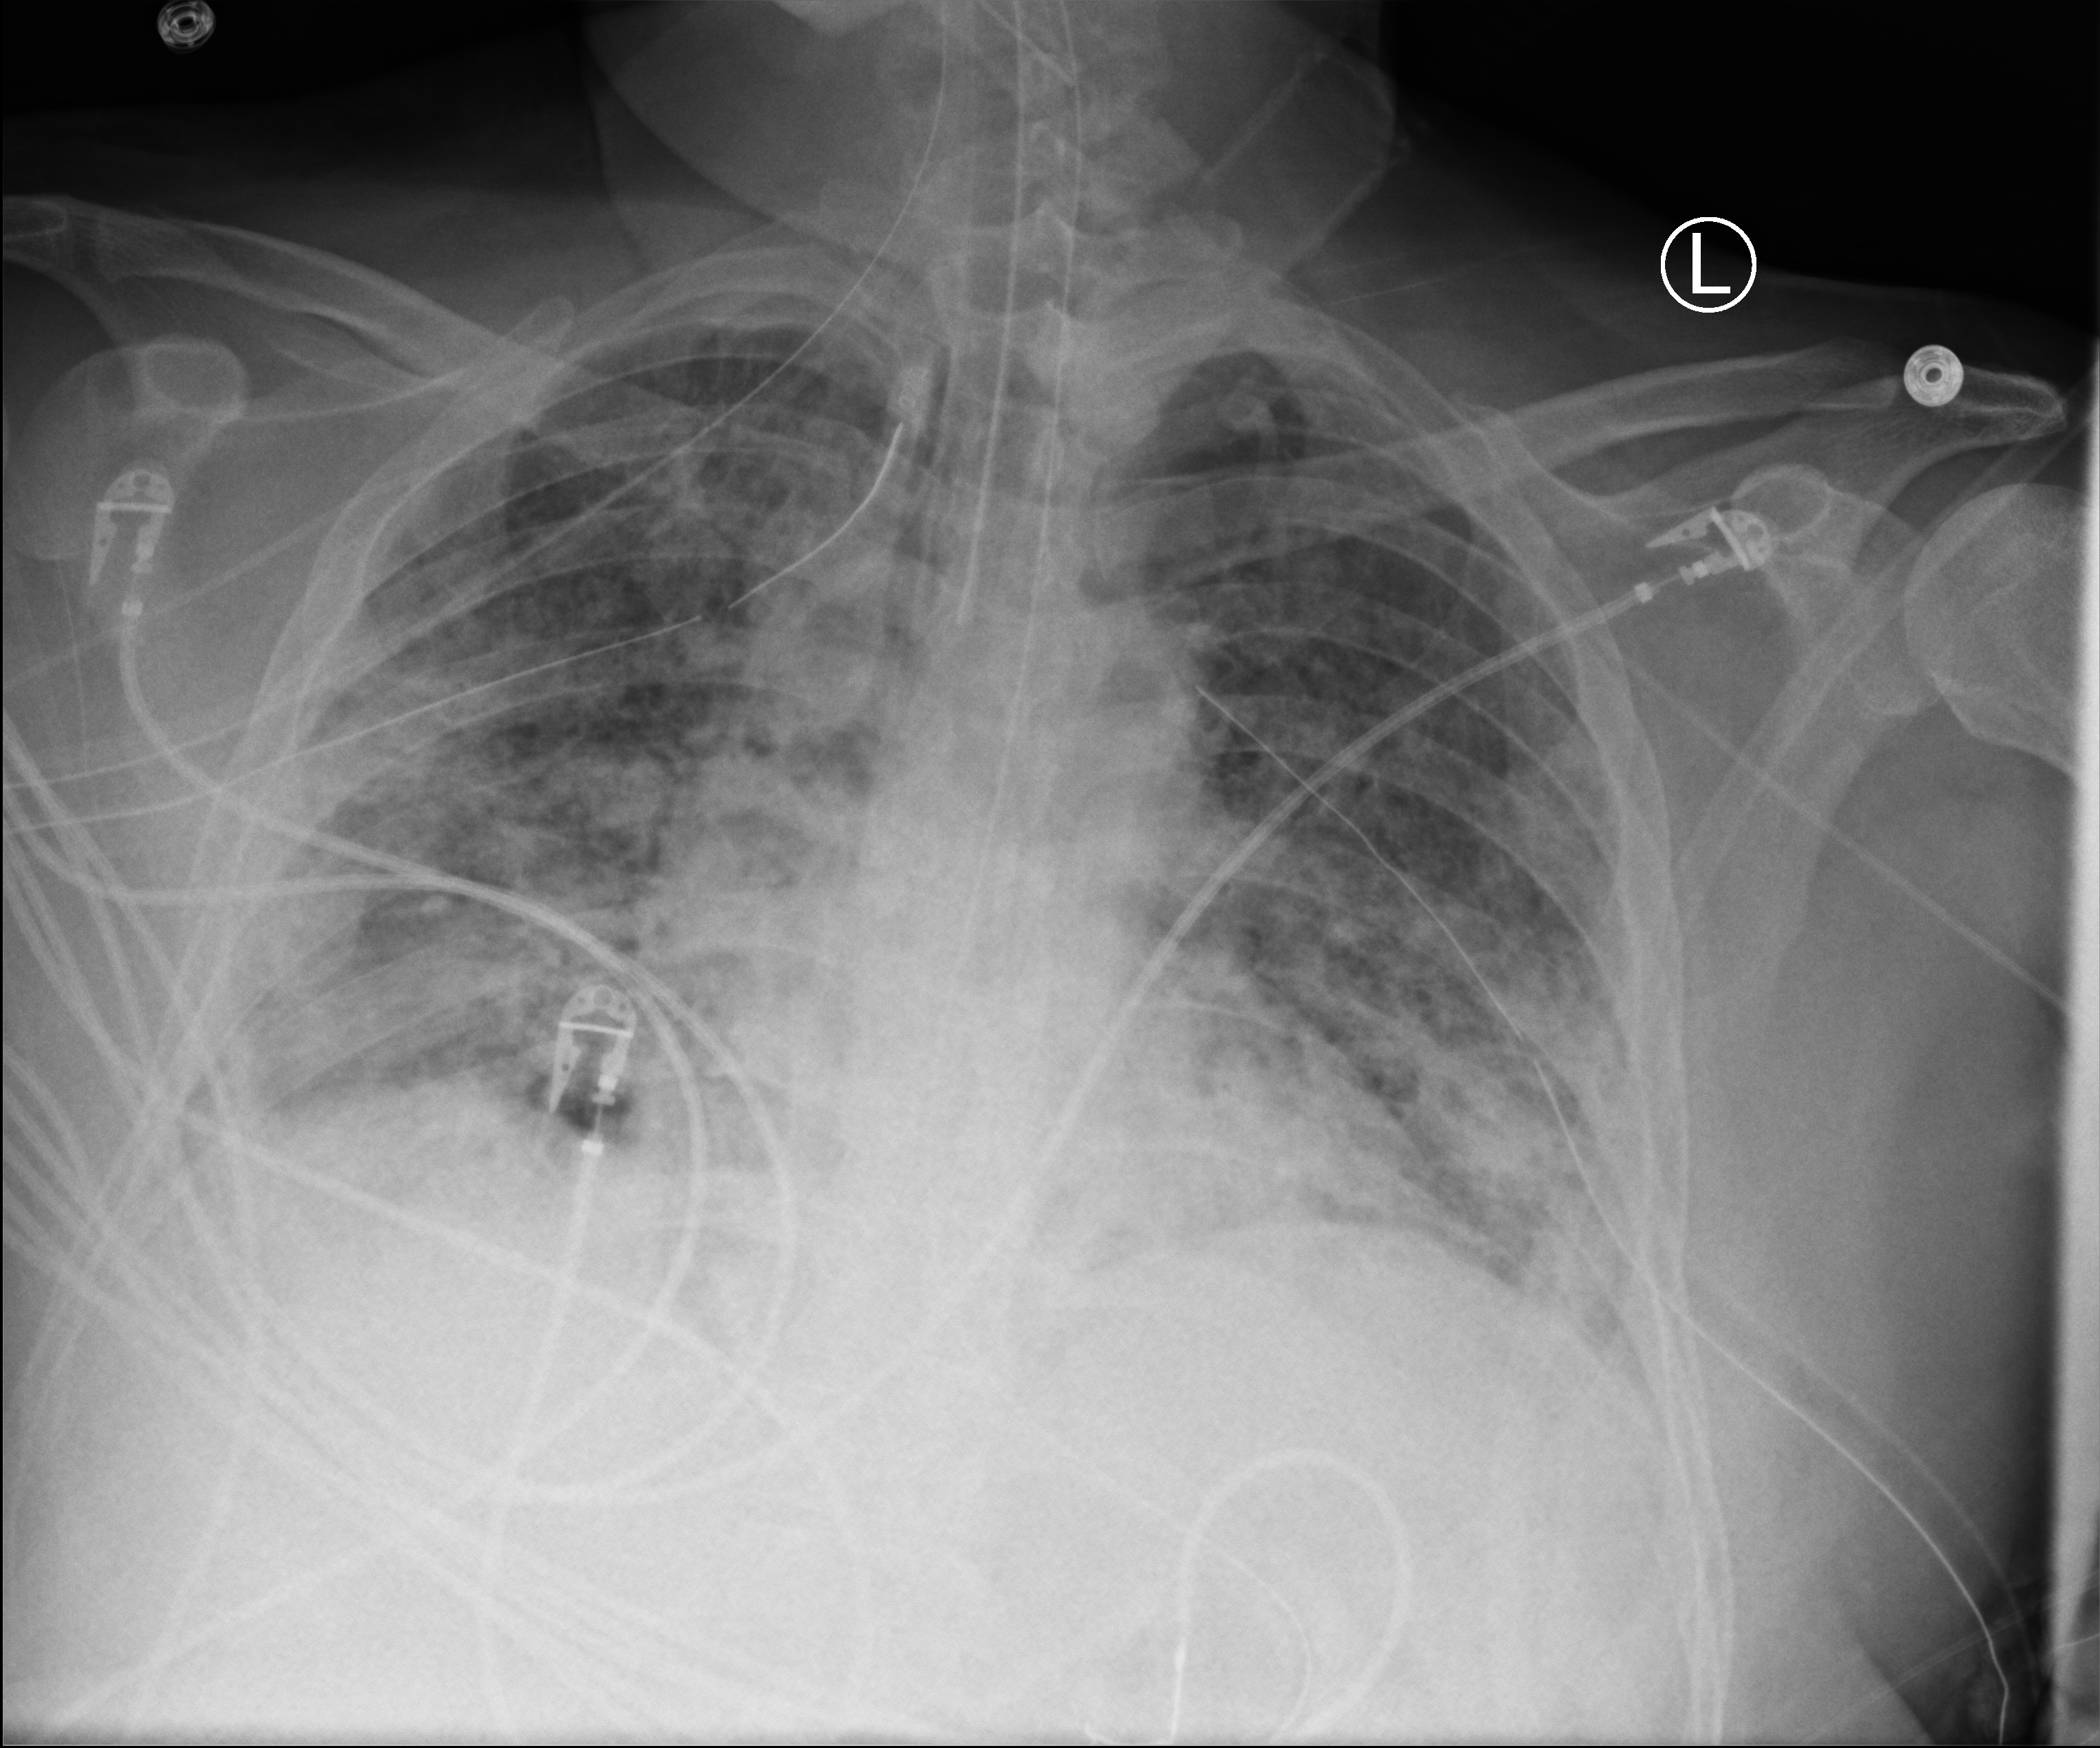
Portable chest radiograph; anteroposterior (AP) projection. Patient hospitalised with COVID-19; male, aged 18–59 years.
Hospital-stay facts (about this admission, not read from this image; timing relative to this image not recorded): other chronic lung disease (admission record): no; mechanically ventilated during this hospital stay: yes; diabetes (admission record): yes.